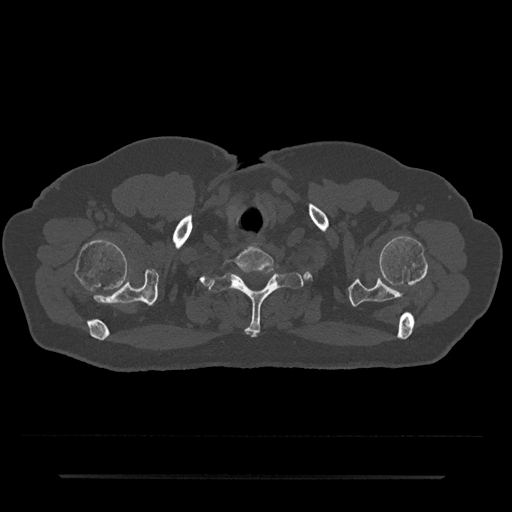
CT including the spine, one axial slice. Position 650 of 797 along the scan axis. Reconstruction kernel Br40s/3. Bone window (W 1800 / L 400 HU). 0.5 mm slice thickness. 512 × 512 image matrix. Male patient, age 69 years. From the clinical record (not read from this slice): primary cancer: prostate.
Outlined on this slice (semi-automatic segmentation, software-assisted and operator-edited):
- T1 vertebra: bounding box (x1, y1, x2, y2) in pixels: (208, 268, 304, 336)